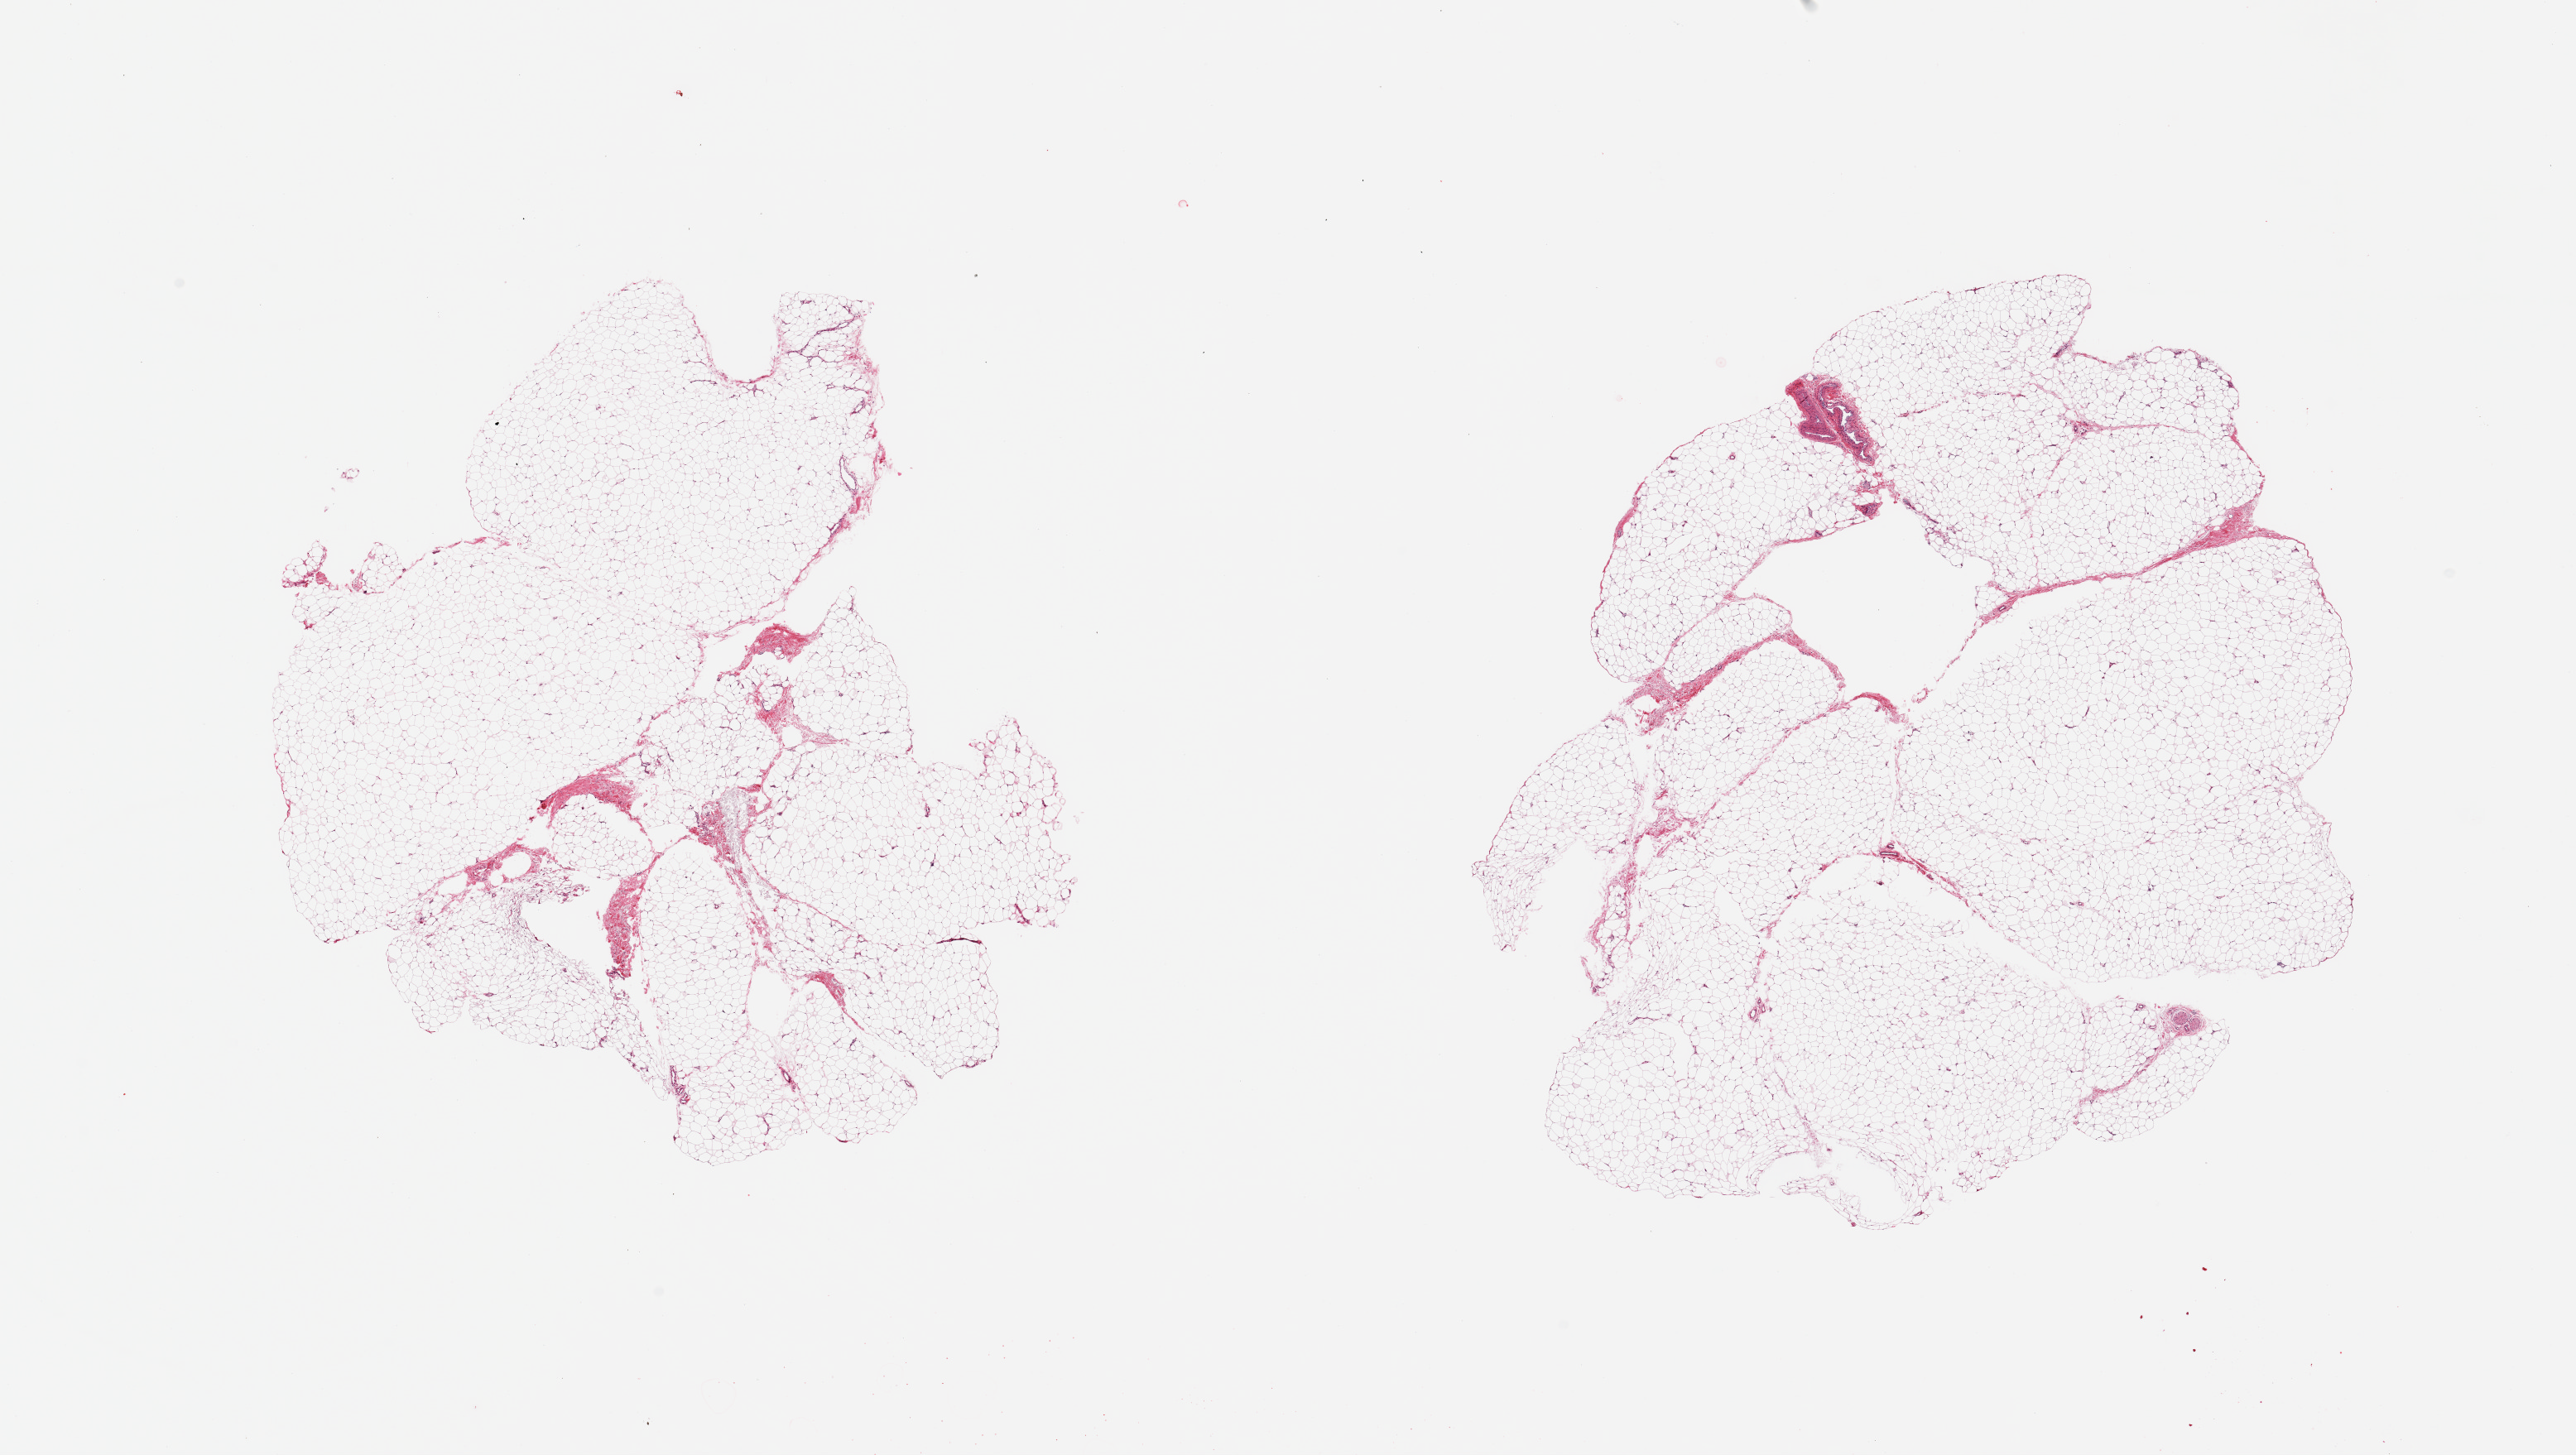
Whole-slide image, H&E stain, brightfield — low-resolution overview of the scanned area, about 24.6 x 13.9 mm (slide scanned at 20x); PAXgene-fixed, paraffin-embedded tissue; sampled site (target tissue): adipose tissue; donor tissue sample. Donor sex: female.
• reviewer comment on this tissue sample: 2 pieces; <5% fibrovascular content